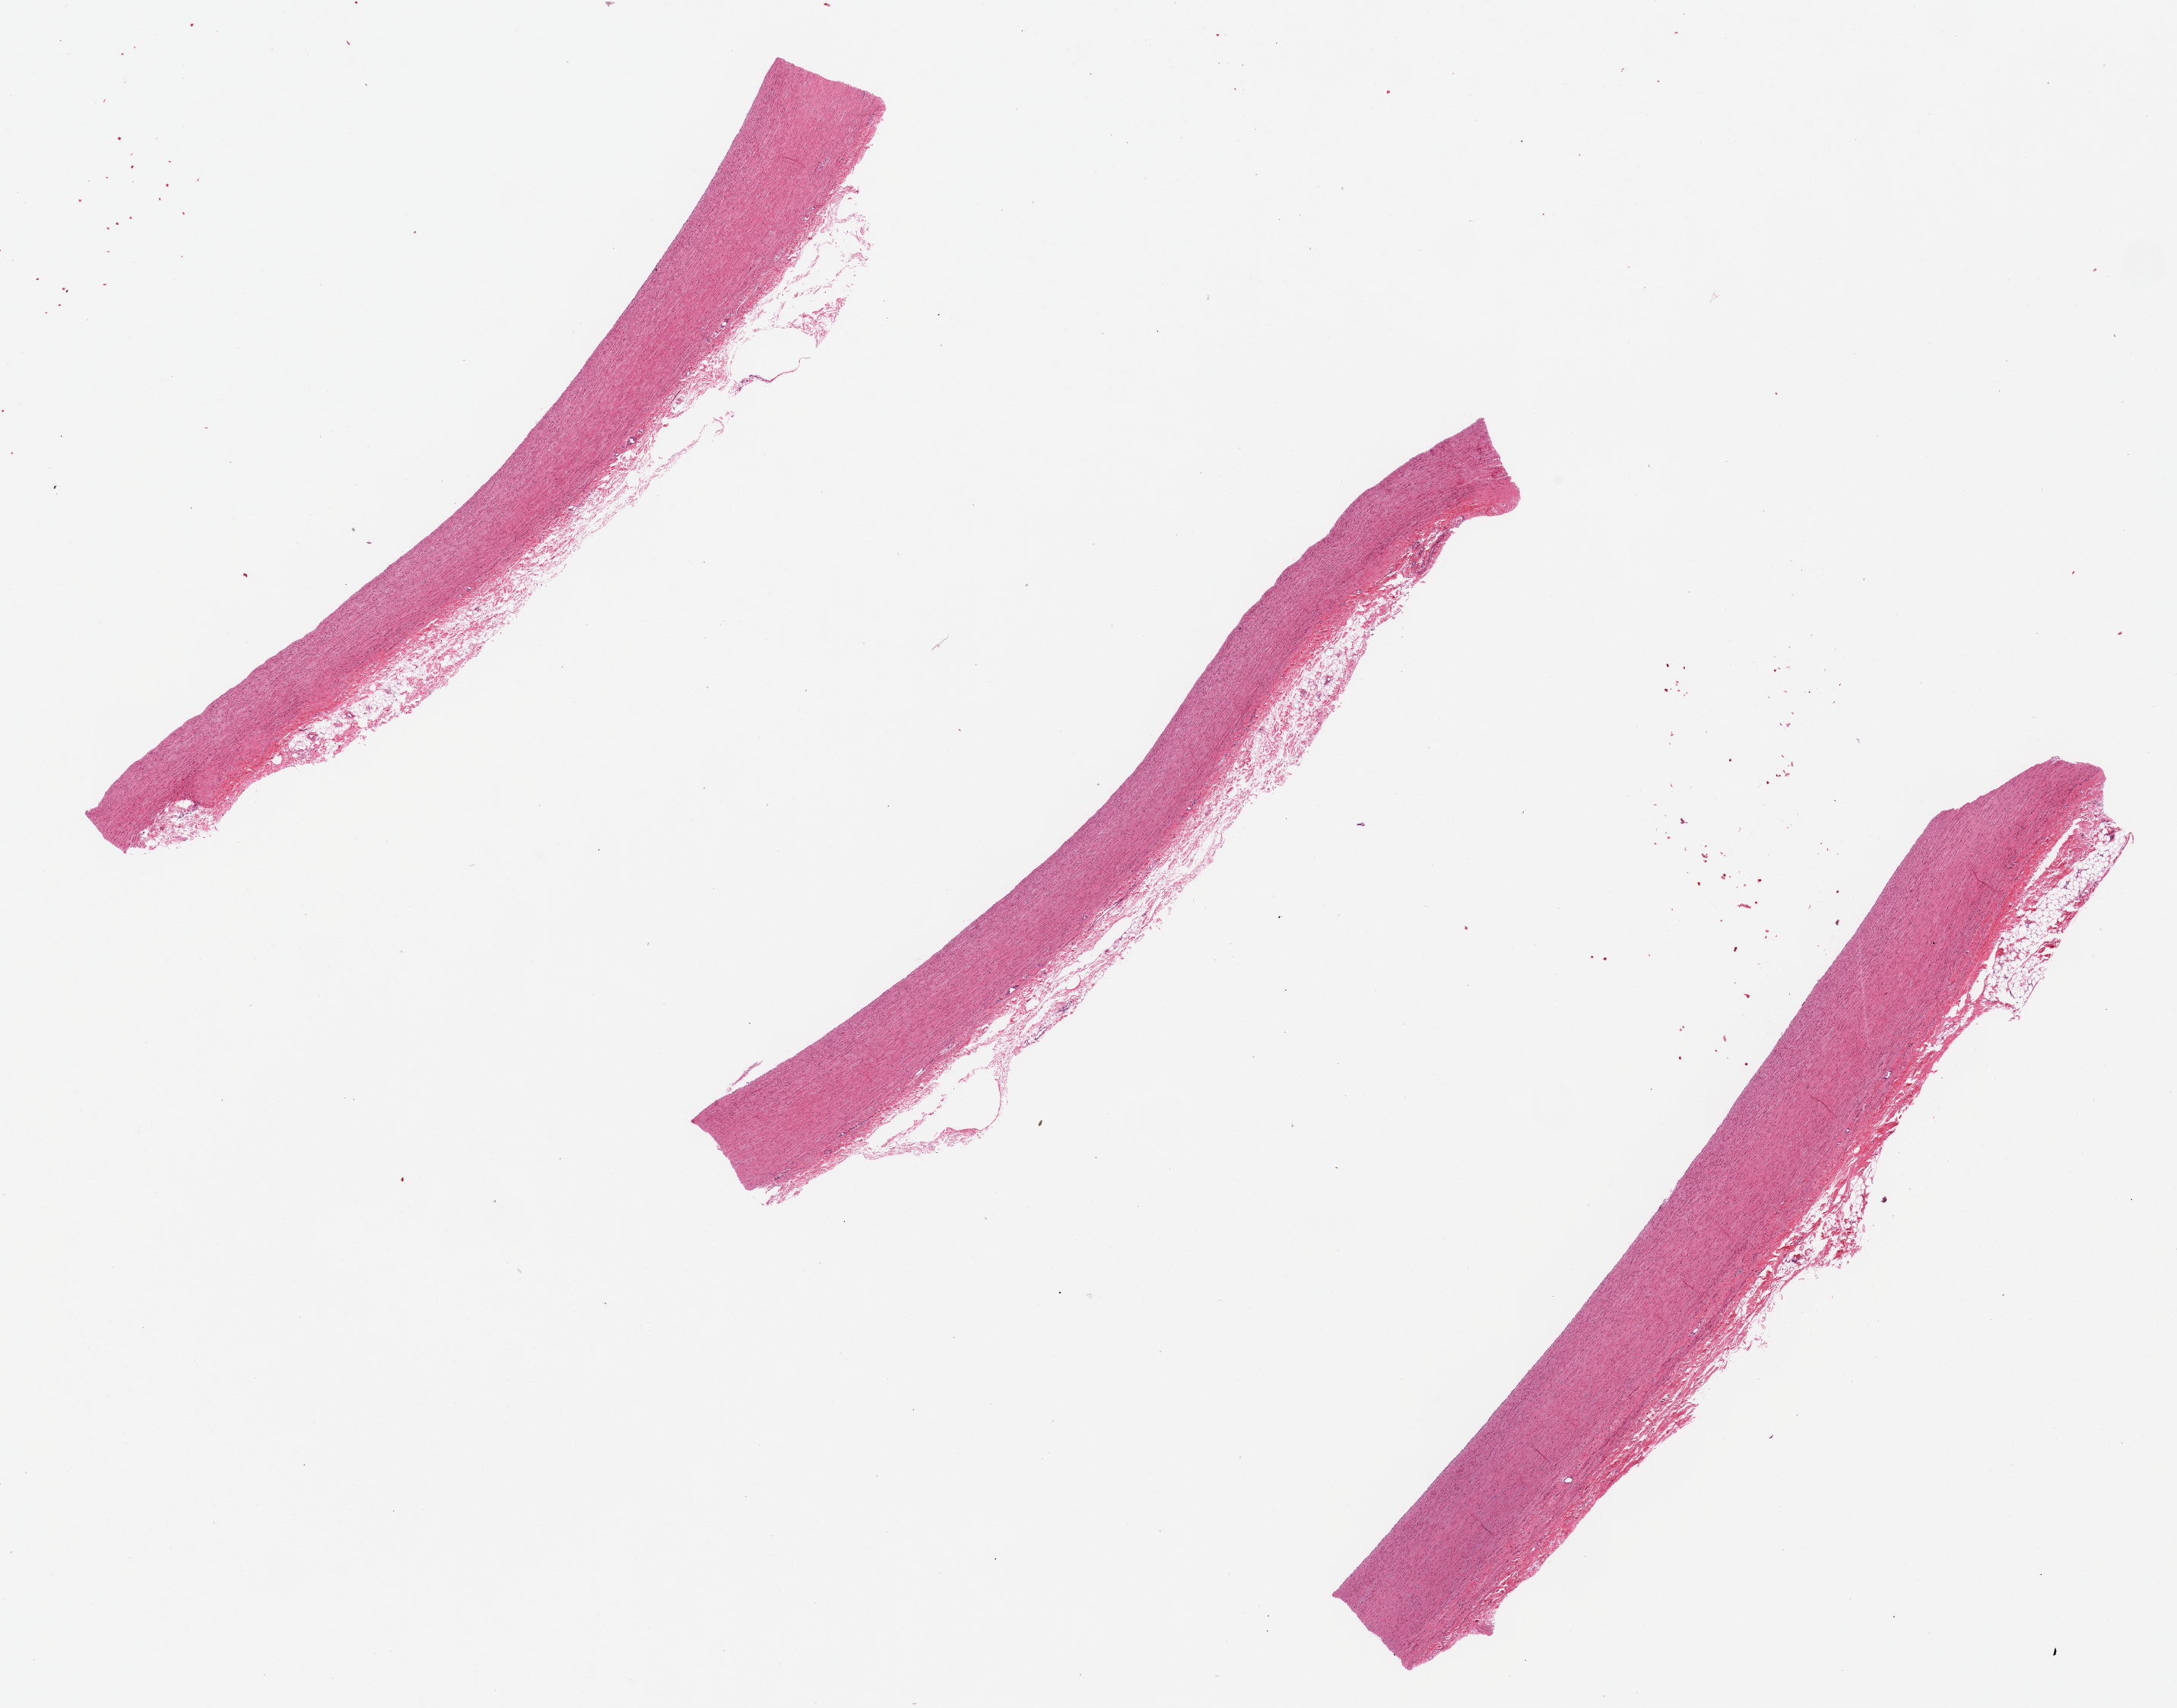
H&E whole-slide image, brightfield — whole scanned area (about 22.6 x 17.8 mm) shown as a low-resolution overview, PAXgene-fixed paraffin-embedded (PFPE) section, target tissue: aorta, tissue donor sample.
- reviewer comment on this tissue sample: 3 pieces